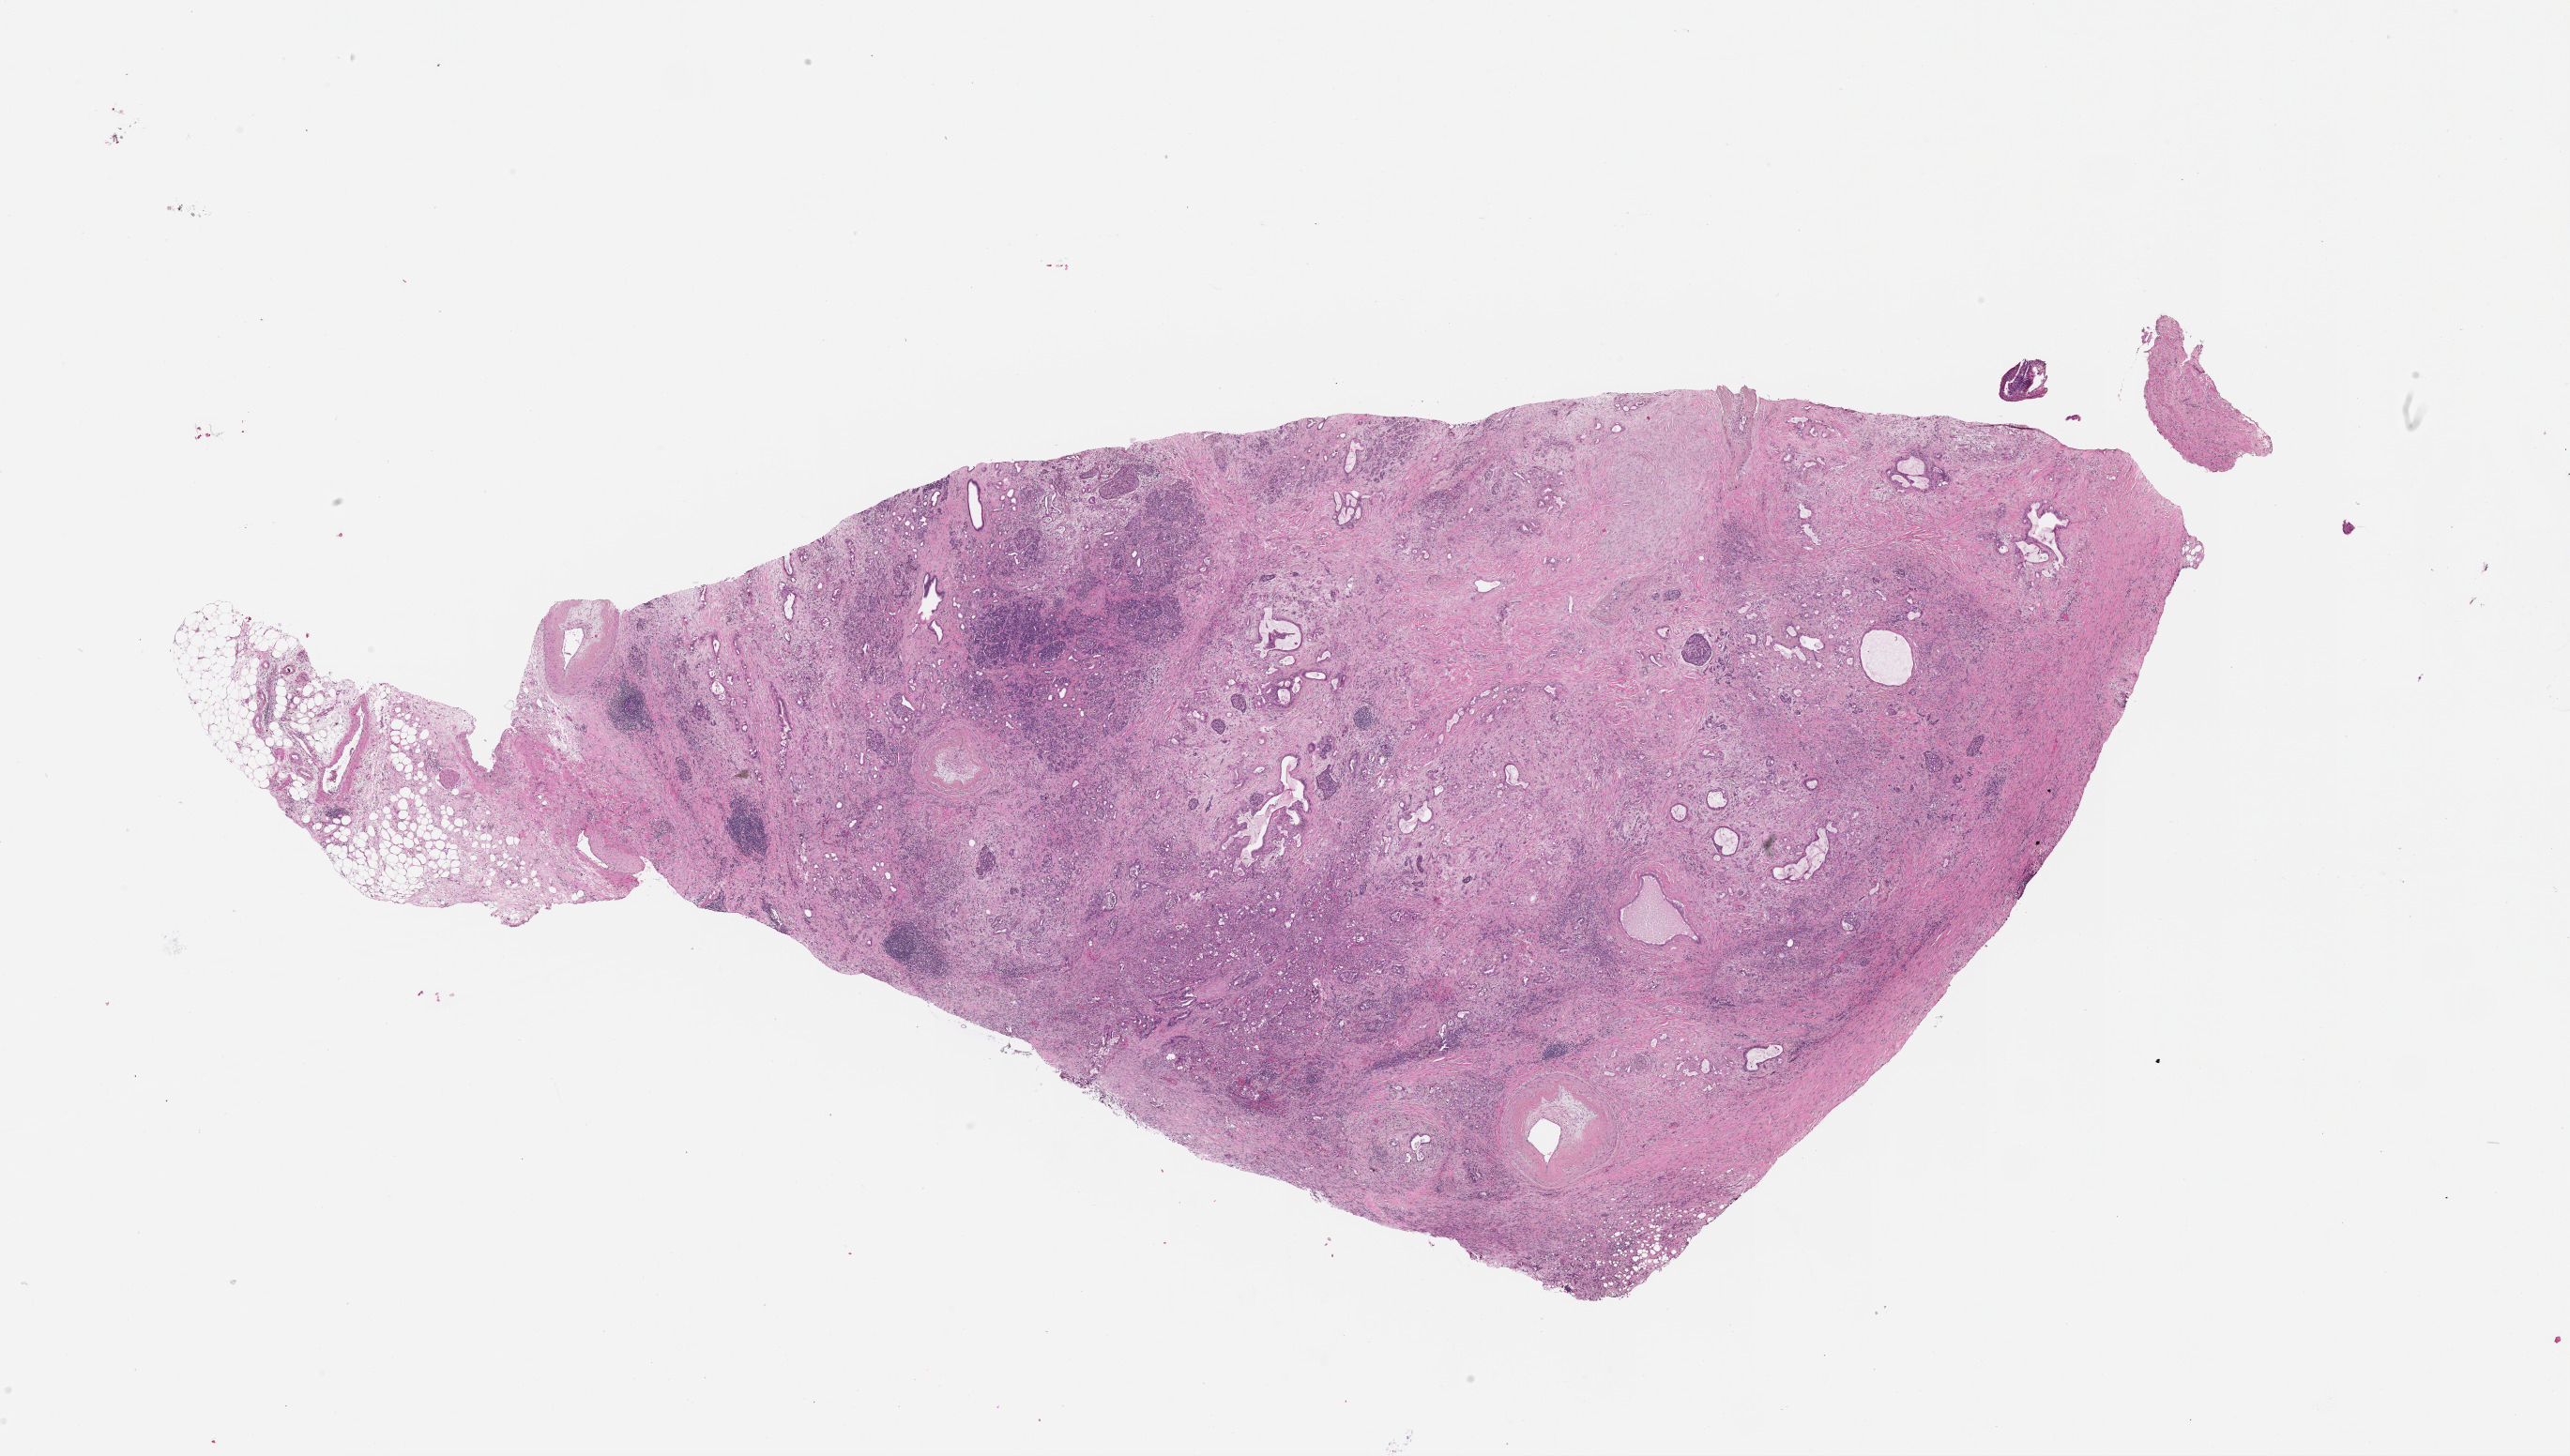
Hematoxylin and eosin (H&E) stained whole-slide image — a low-resolution overview of the entire scanned area, about 22.0 x 12.5 mm. Tumour tissue sample, pancreas. Male, 78 y/o. Histologic grade: G2 (moderately differentiated).
Primary tumour site (as recorded): tail. AJCC pathologic stage: III. Diagnosis: Infiltrating duct carcinoma, NOS.